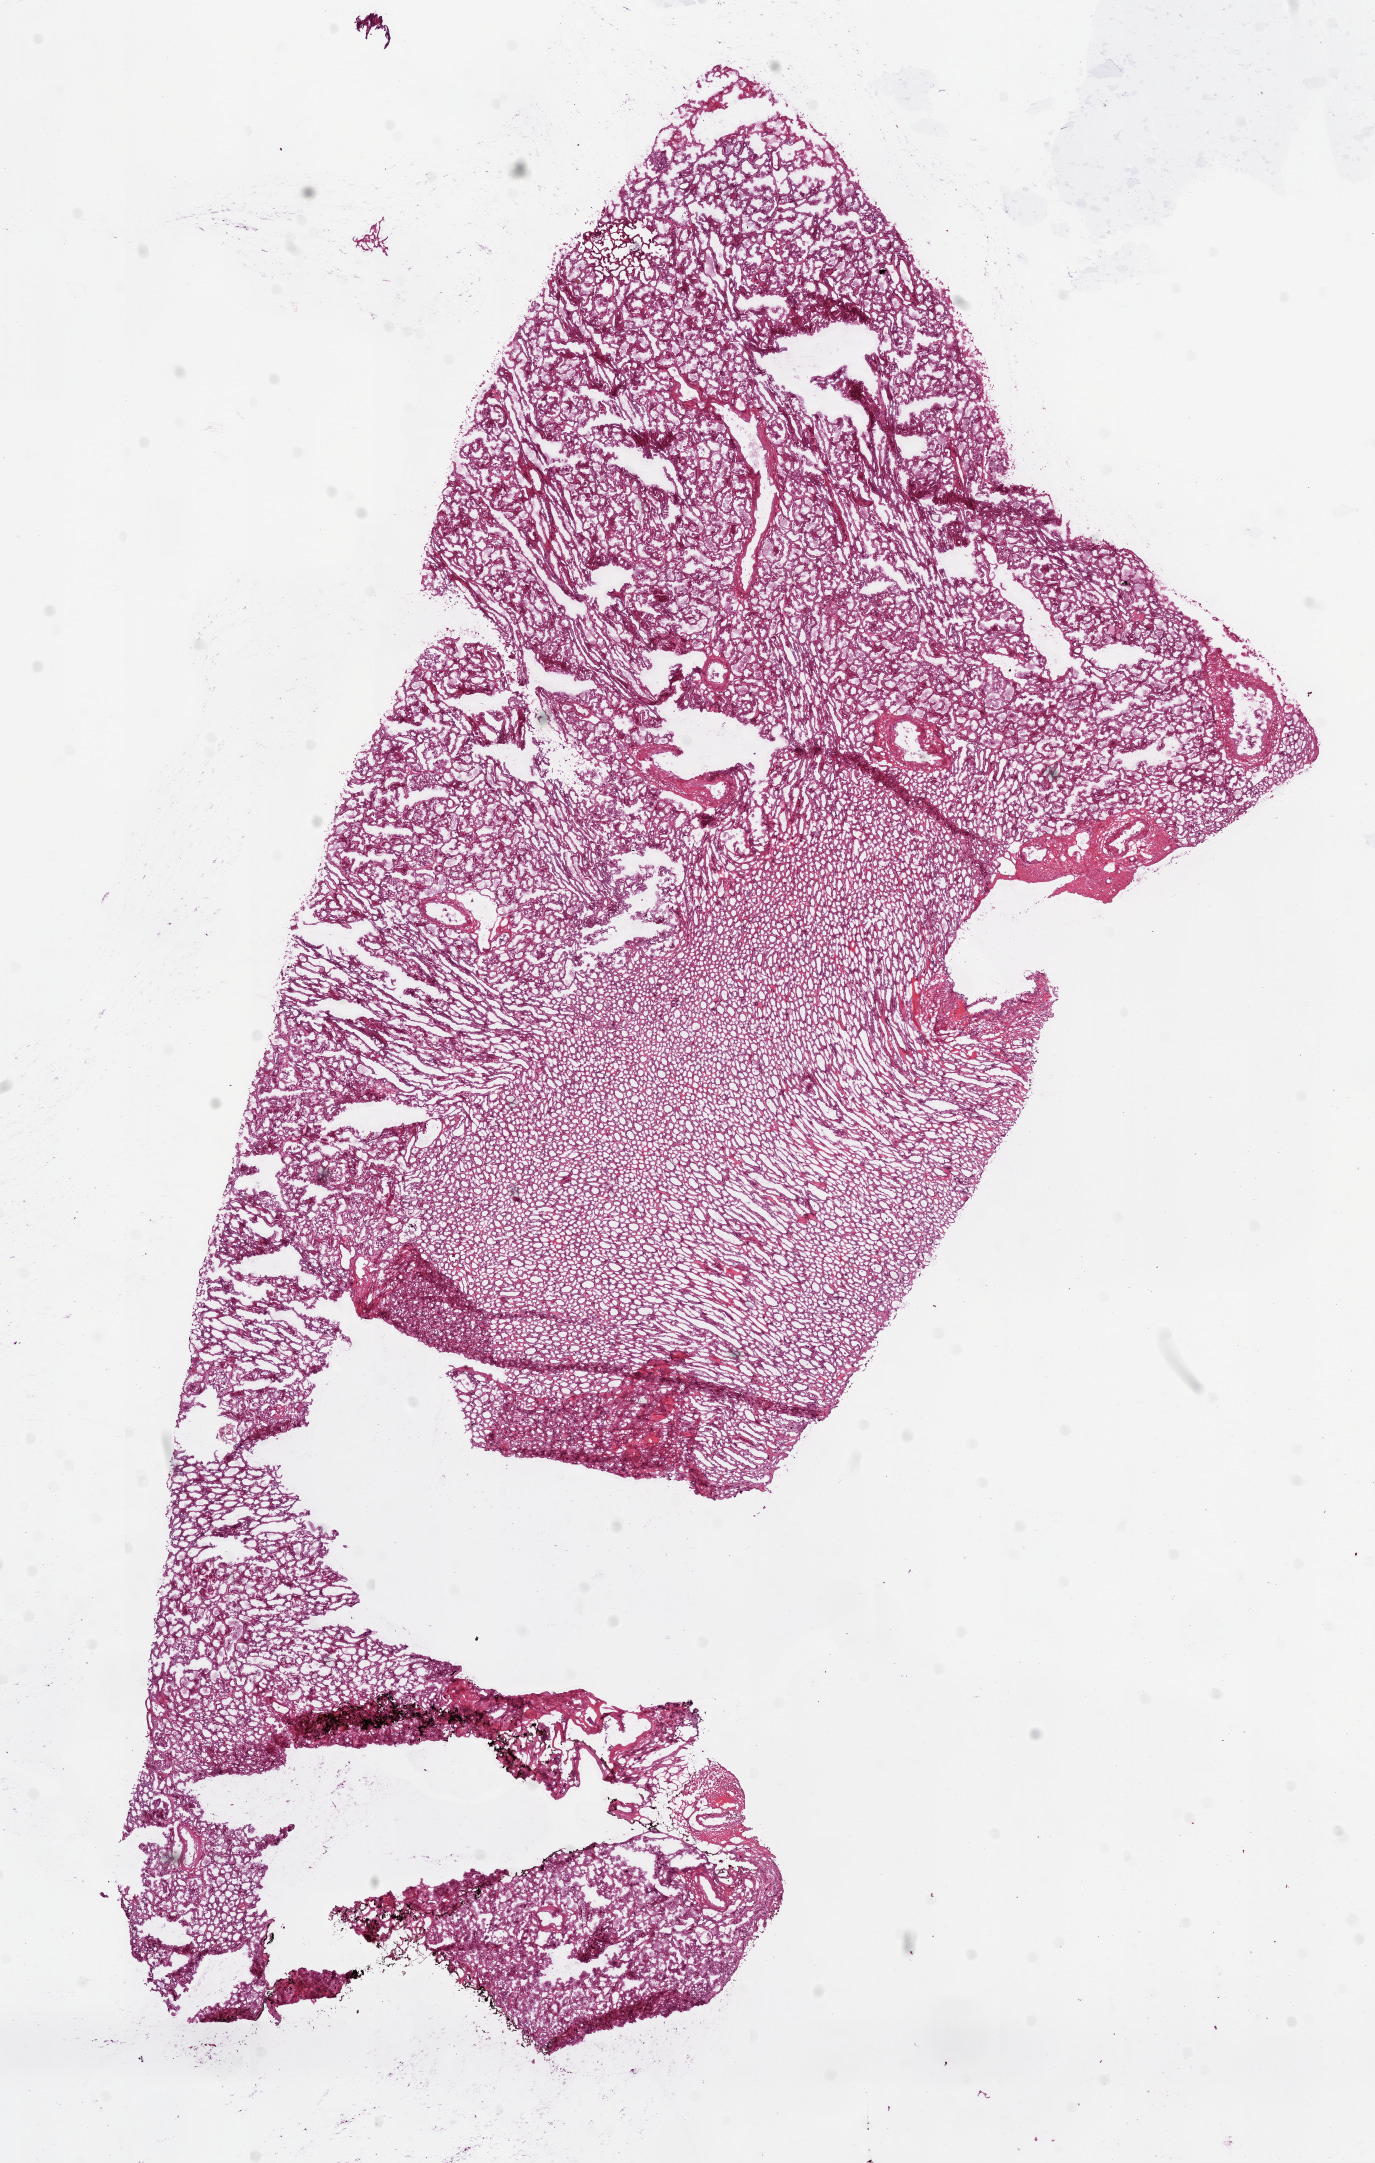
Hematoxylin and eosin (H&E) stained whole-slide image — a low-resolution overview of the entire scanned area, about 11.0 x 17.4 mm; frozen section from the bottom of the tissue portion; kidney, solid tissue normal (non-tumour tissue) sample. Male patient; age at initial diagnosis 65 years.
* this section: solid tissue normal sample (biorepository sample class)
* patient diagnosis: Clear cell adenocarcinoma, NOS